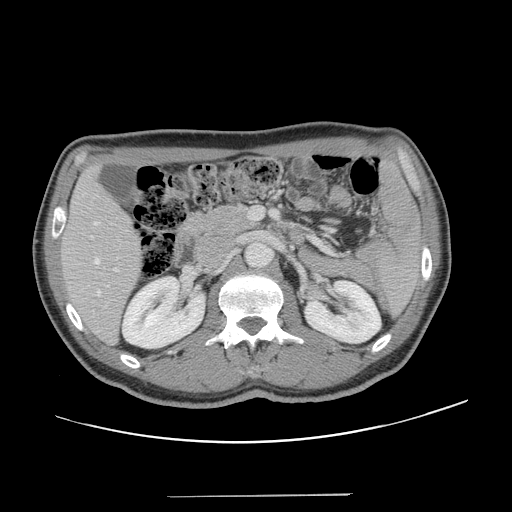
Contrast-enhanced abdominal CT, one axial slice. Position 66 of 131 along the scan axis. Intravenous contrast given. Soft-tissue window (W 400 / L 40 HU). 512 × 512 image matrix, field of view 403 × 403 mm. Male patient, age 60 years. From the clinical record (not read from this slice): diagnosis: colorectal cancer liver metastases, imaged before liver resection; multiple liver metastases: no; largest metastasis: 2.5 cm; disease in both lobes: no.
Outlined on this slice (manually delineated by an expert):
- hepatic veins: bounding box [x1, y1, x2, y2] px = [94, 222, 101, 296]
- liver: [62, 170, 142, 343]
- planned liver remnant (the part of the liver to remain after resection): [62, 170, 142, 343]